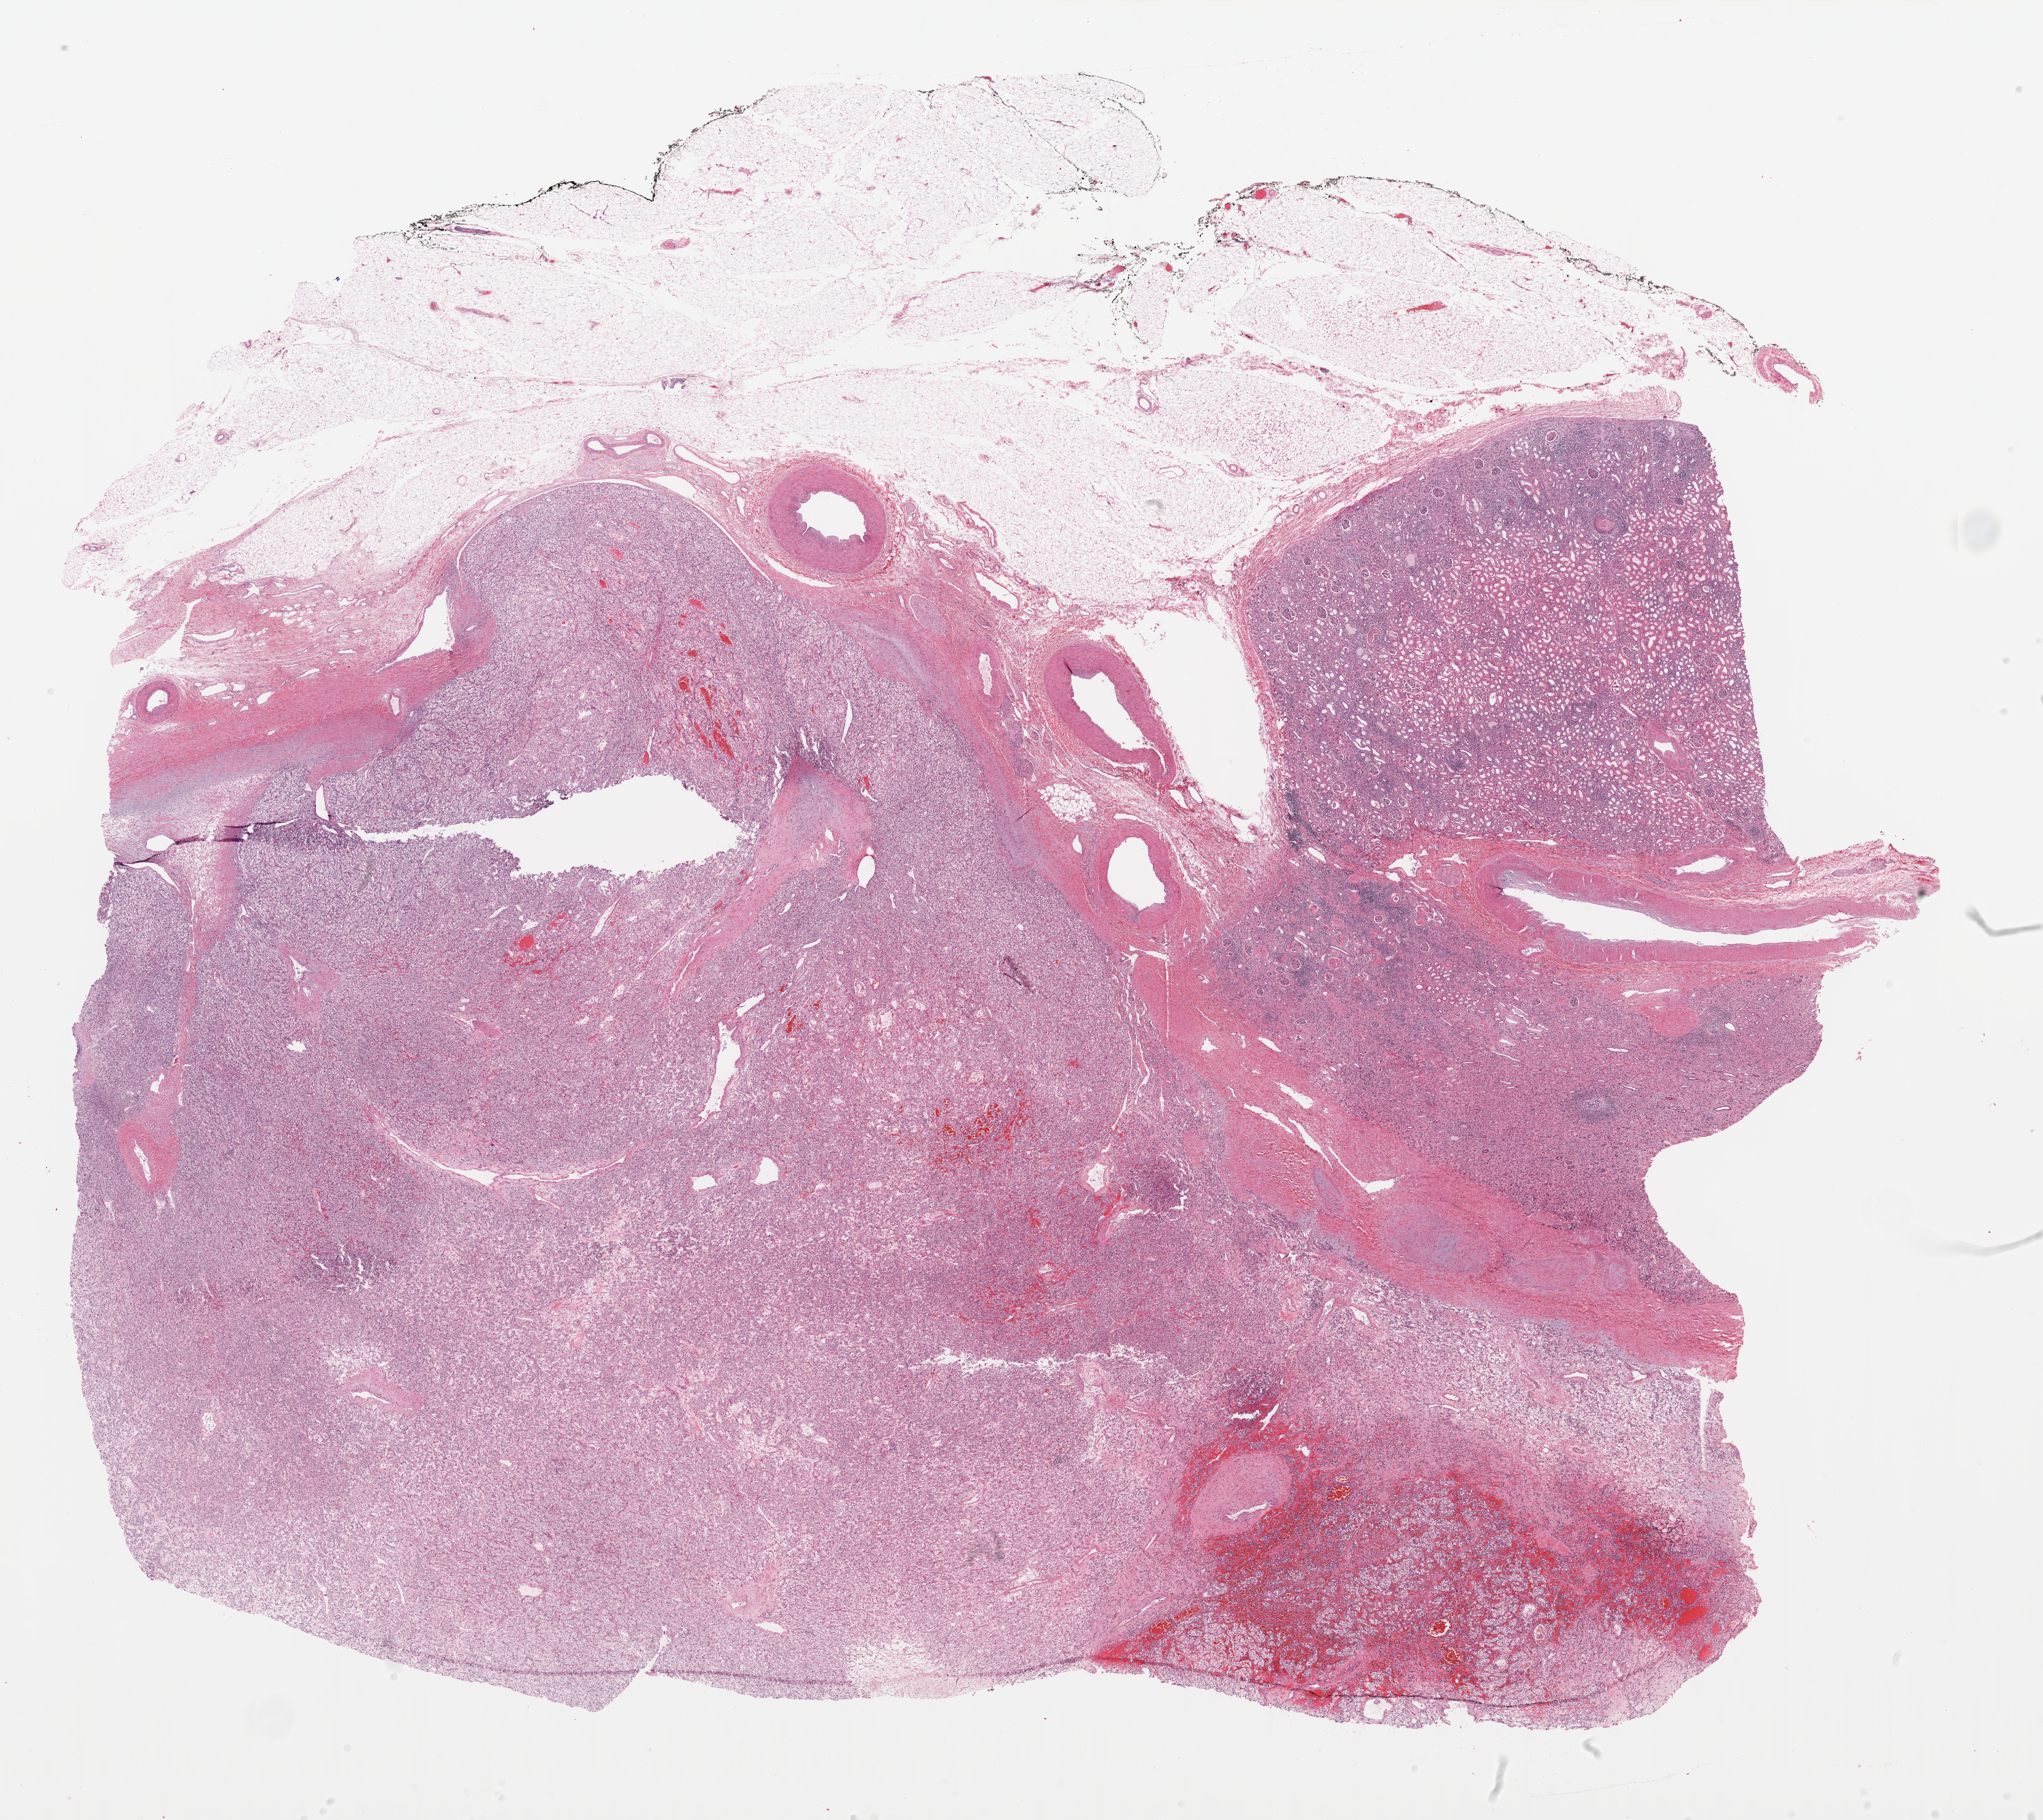
H&E whole-slide image, shown as a low-resolution overview of the whole scanned area (about 24.1 x 21.4 mm, slide scanned at 20x). Formalin-fixed paraffin-embedded (FFPE) diagnostic section. Primary tumour sample from the kidney. Female patient; age at initial diagnosis 51 years.
Pathologic diagnosis: Clear cell adenocarcinoma, NOS.